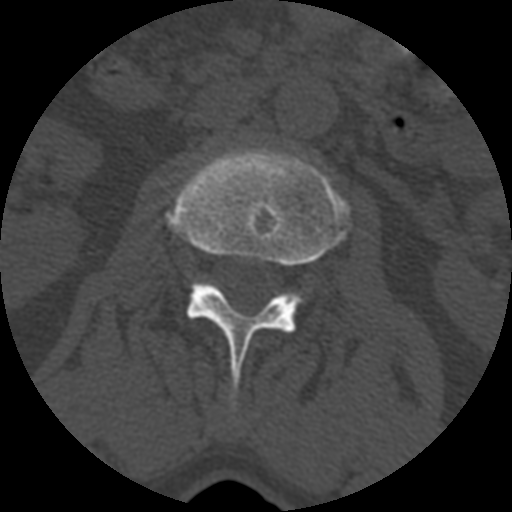
CT including the spine, one axial slice. Position 330 of 399 along the scan axis. Bone window (W 1800 / L 400 HU). 1.25 mm slice thickness. 512 × 512 image matrix, field of view 160 × 160 mm. Patient age 71 years. From the clinical record (not read from this slice): primary cancer: prostate.
Structures marked on this image (semi-automatic segmentation, software-assisted and operator-edited):
- L2 vertebra: bounding box (x1, y1, x2, y2) in pixels: (167, 147, 351, 411)